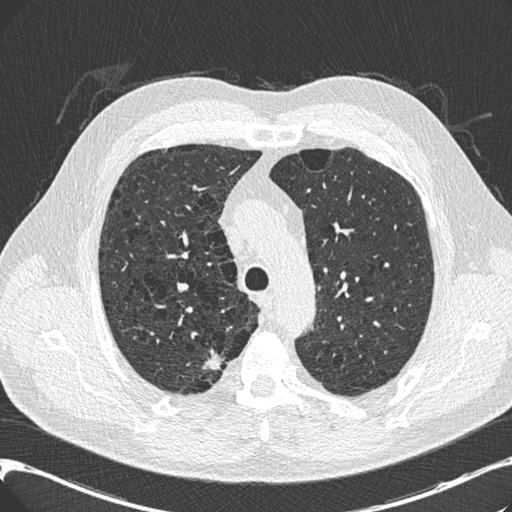
Axial slice from a low-dose chest CT screening exam, third screening round (two years after baseline), lung window (W 1500 / L -600 HU), standard (soft-tissue) reconstruction kernel (B30f), 512 × 512 image matrix, field of view 367 × 367 mm. Male participant, aged 68 years at enrolment.
Expert reader's lesion annotation, bounding box <189,346,236,384> (left, top, right, bottom; pixels). The screening reader recorded 3 non-calcified nodules or masses ≥4 mm on this exam (right upper lobe, right upper lobe, left lower lobe); which of them this box marks is not recorded.